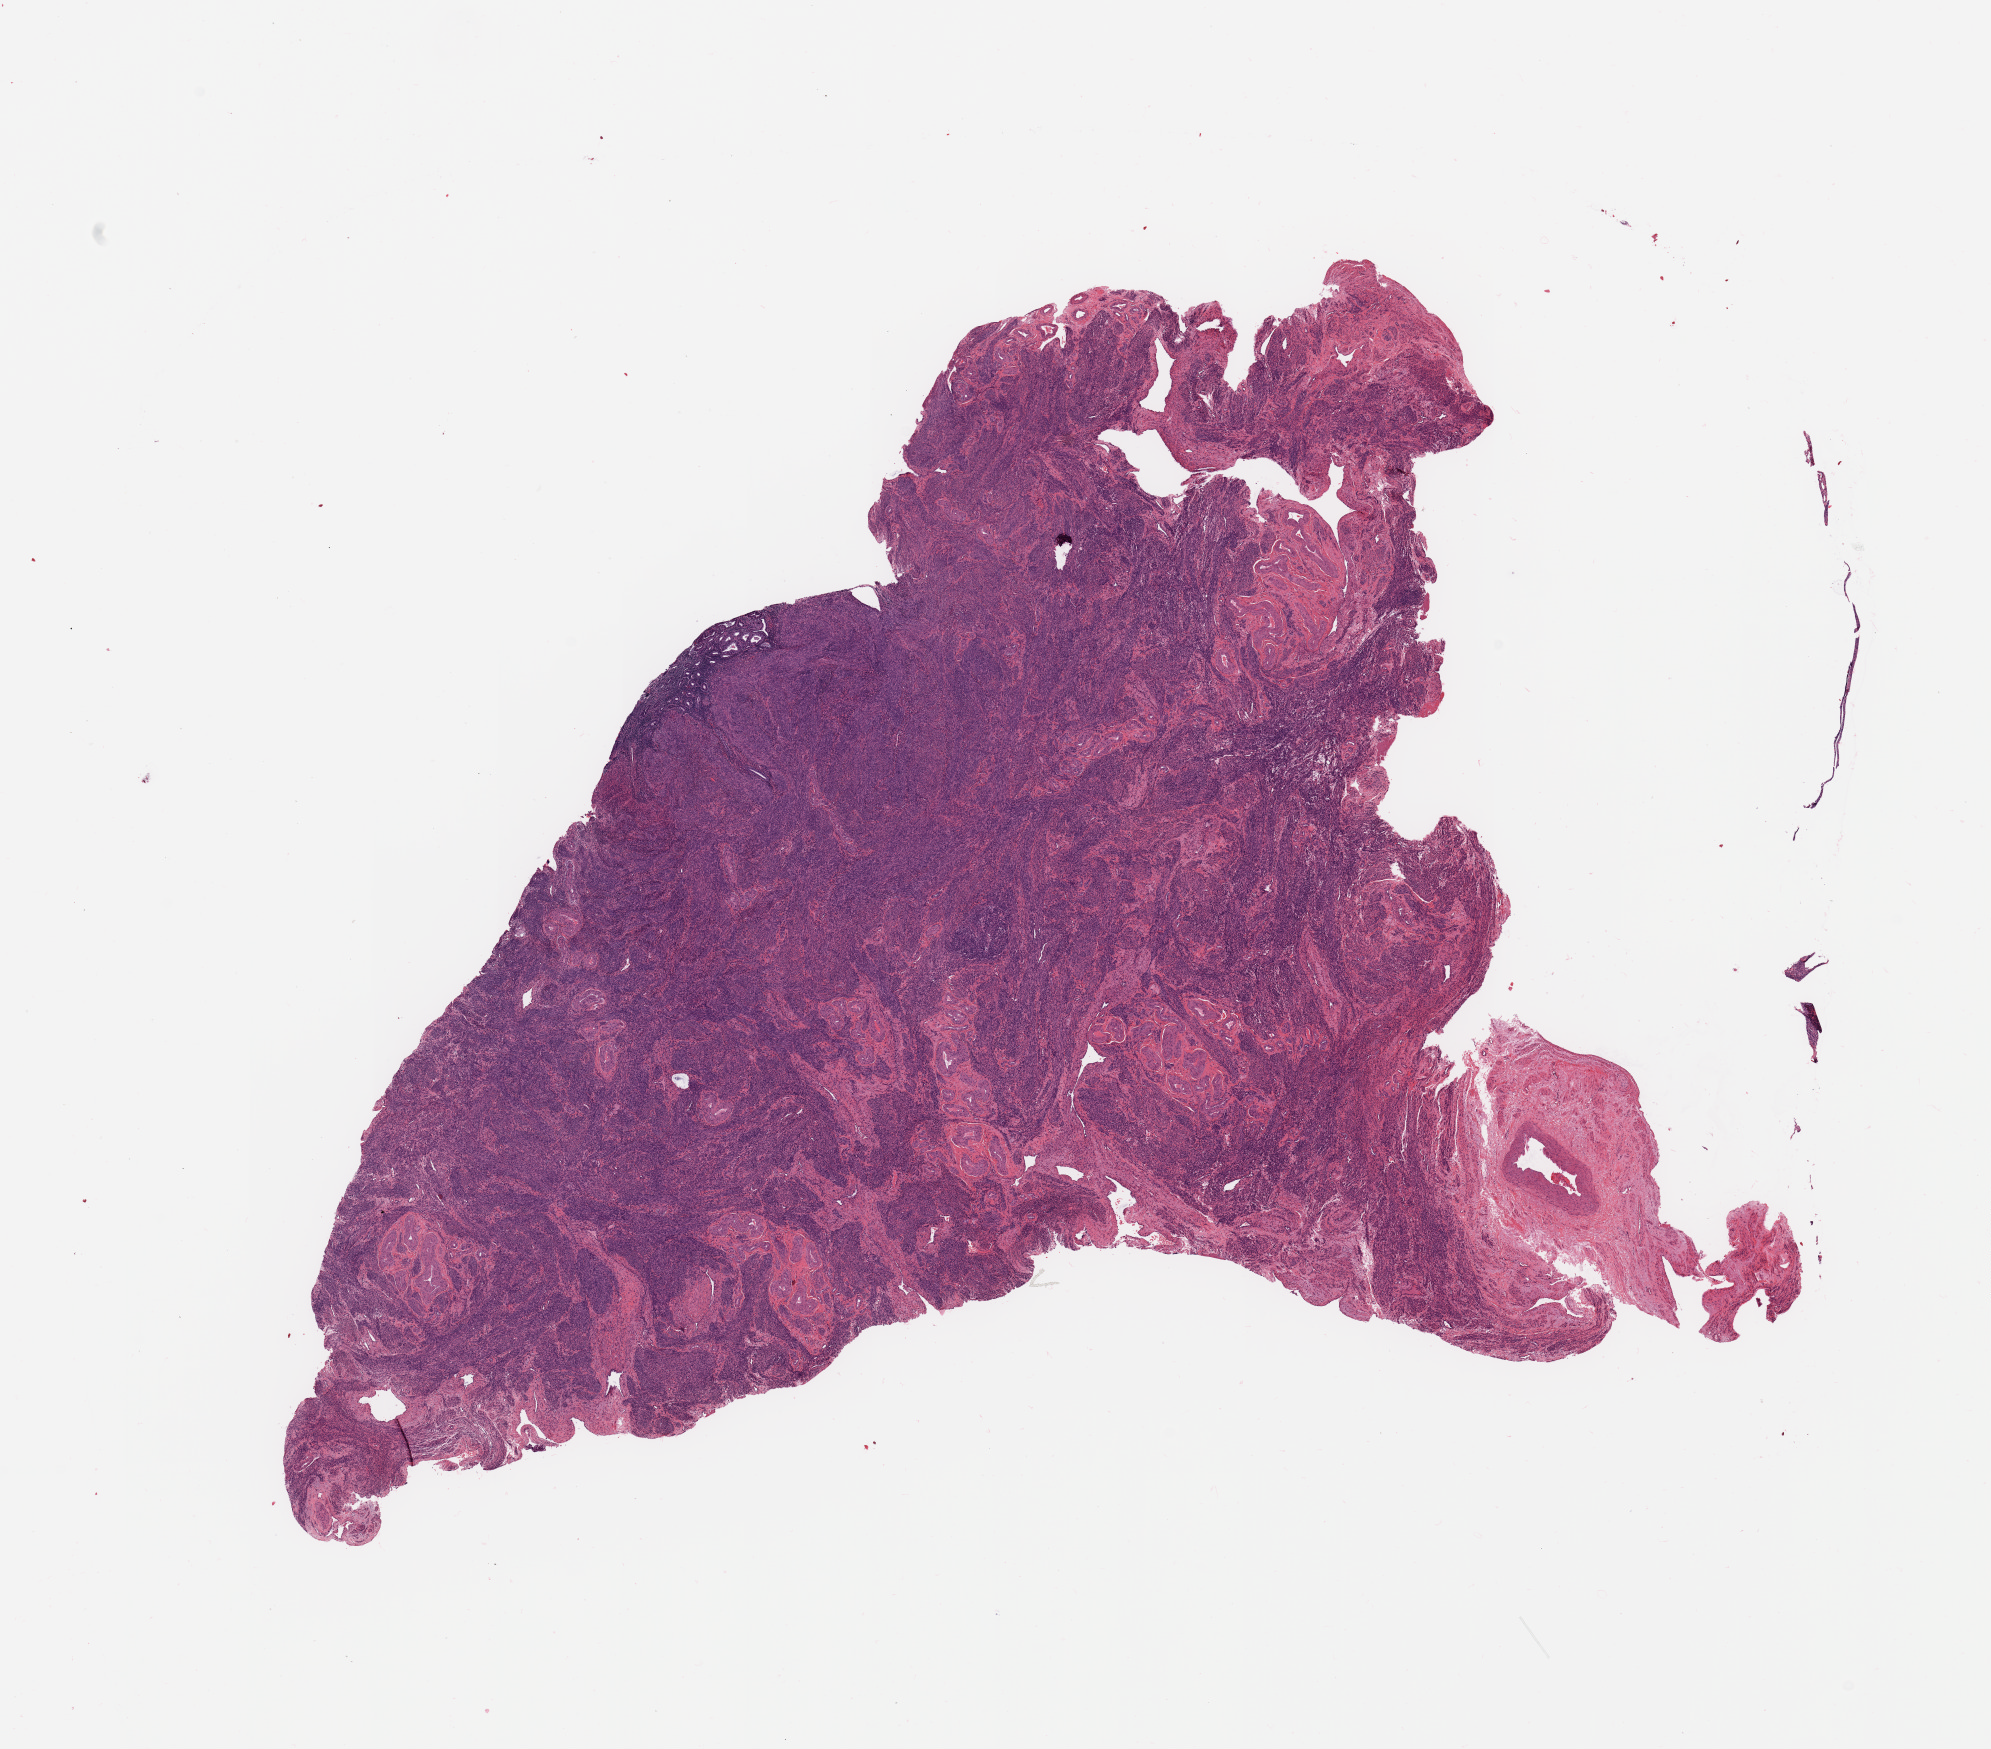
Hematoxylin and eosin (H&E) stained whole-slide image, low-resolution overview of the scanned area, about 15.8 x 13.8 mm (slide scanned at 20x). Normal (non-tumour) tissue sample, sampled site: uterus. 65-year-old female patient.
This section: normal (non-tumour) tissue from the same patient. Patient diagnosis: Endometrioid adenocarcinoma, NOS.